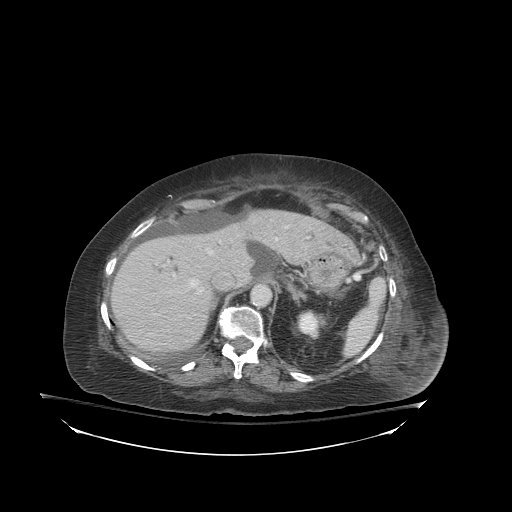
Contrast-enhanced abdominal CT (liver protocol), one axial slice; slice 61 of 81 in the series (ordered by position); reconstruction kernel STANDARD; soft-tissue window (W 400 / L 40 HU); 512 × 512 image matrix, field of view 500 × 500 mm. Case-level facts recorded for this patient, not image findings: diagnosis: hepatocellular carcinoma (patient treated with transarterial chemoembolisation; whether this scan precedes or follows treatment is not stated here); TNM stage (as recorded): Stage-I; Child-Pugh class: B.
Structures marked on this image (semi-automatically segmented with operator editing):
- liver parenchyma outside the tumour (the mass and vessels are separate outlines, so this box may not span the whole liver): bounding box [x1, y1, x2, y2] px = [110, 210, 358, 354]
- liver vessels: [174, 227, 287, 287]